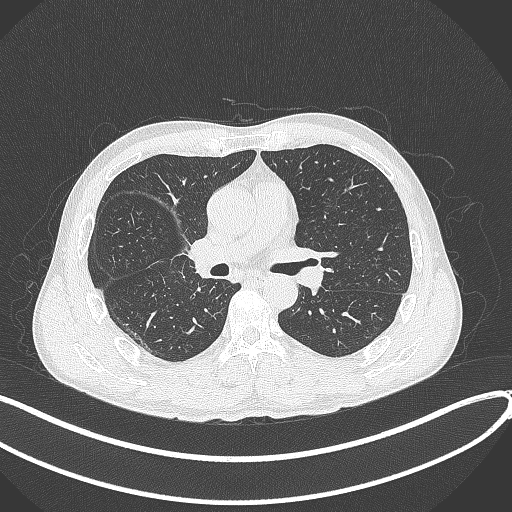
Chest CT, one axial slice; reconstruction kernel B70f; lung window (W 1500 / L -600 HU); 1 mm slice thickness; 512 × 512 image matrix, field of view 400 × 400 mm. Male patient, age 53 years. Case-level facts recorded for this patient, not image findings: clinical TNM (as recorded): T1b N0 M0.
Outlined on this slice (rectangle marked by the reading radiologist):
- lung tumour (recorded histology: squamous cell carcinoma): bounding box (x1, y1, x2, y2) in pixels: (187, 234, 215, 278)